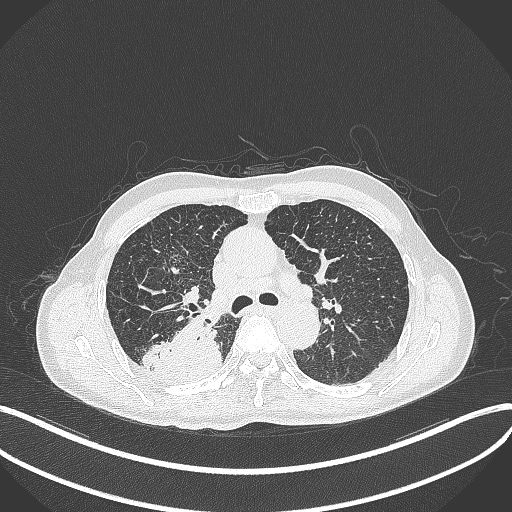
Chest CT, one axial slice. Slice 299 of 428 in the series (ordered by position). Reconstruction kernel B70f. Lung window (W 1500 / L -600 HU). 1 mm slice thickness. 512 × 512 image matrix, field of view 400 × 400 mm. Male patient, age 79 years. From the clinical record (not read from this slice): clinical TNM (as recorded): T3 N0 M0.
Structures marked on this image (bounding box drawn by a radiologist):
- lung tumour (recorded histology: adenocarcinoma): box from (x=143, y=311) to (x=225, y=386) px